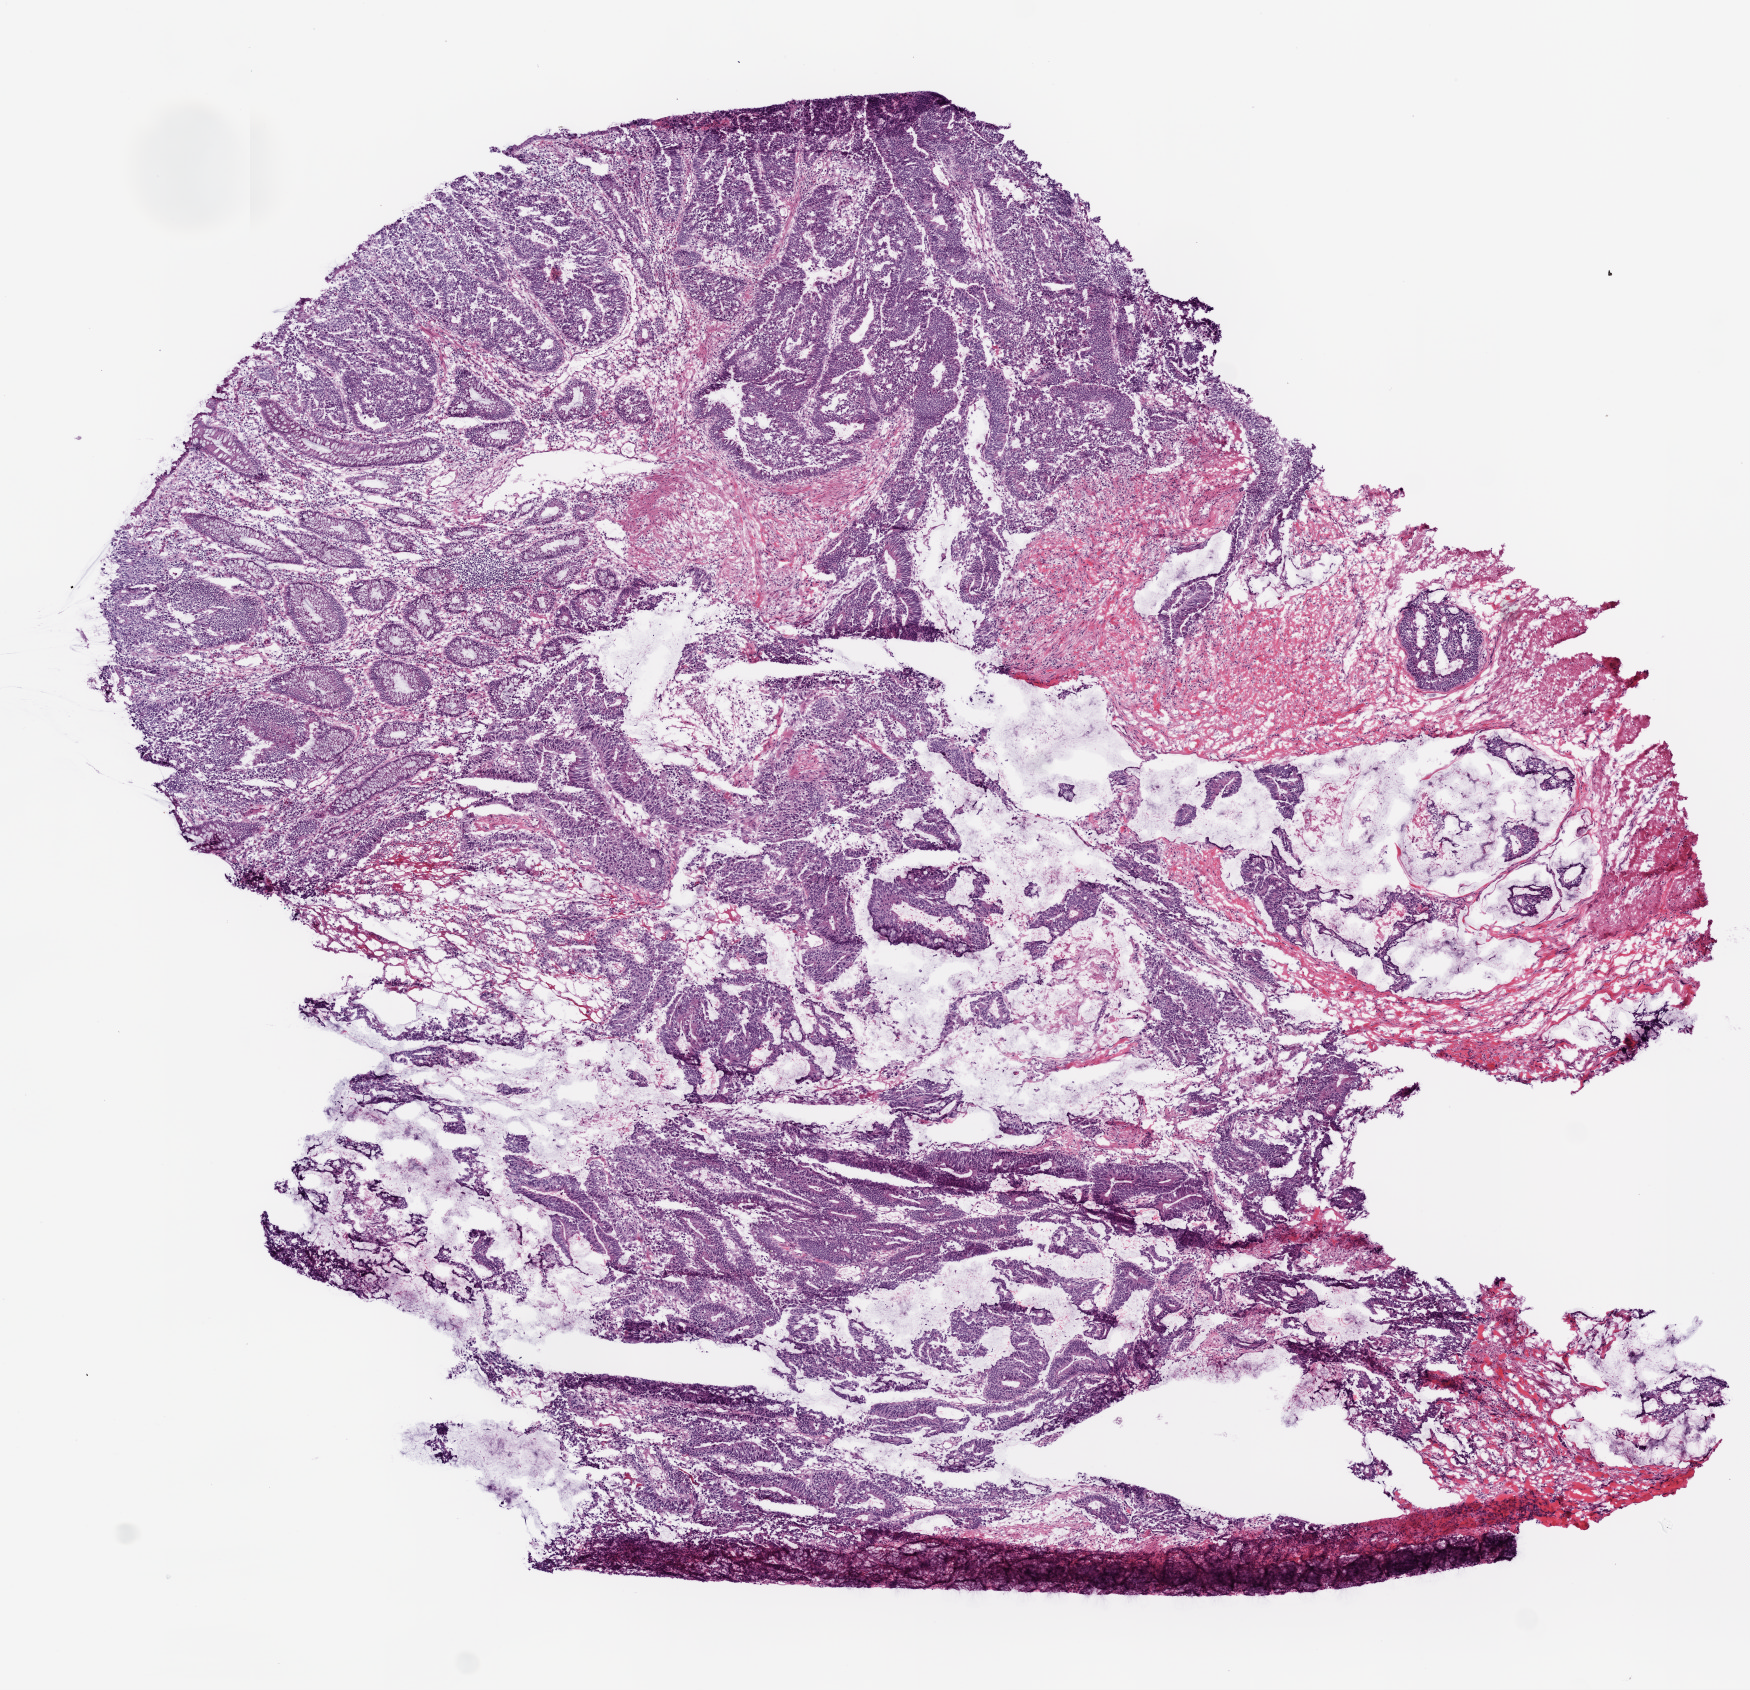
Whole-slide histology image, Hematoxylin and eosin (H&E) stained — a low-resolution overview of the entire scanned area, about 7.0 x 6.8 mm (slide scanned at 20x). Frozen section from the top of the tissue portion. Primary tumour sample from the colon. Patient: female, age at initial diagnosis 47 years. Composition of this section per pathologist review: tumour cells 70%, tumour nuclei 70%, normal cells 10%, stromal cells 15%, necrosis 5%.
- AJCC pathologic stage: IV
- histologic diagnosis: Mucinous adenocarcinoma